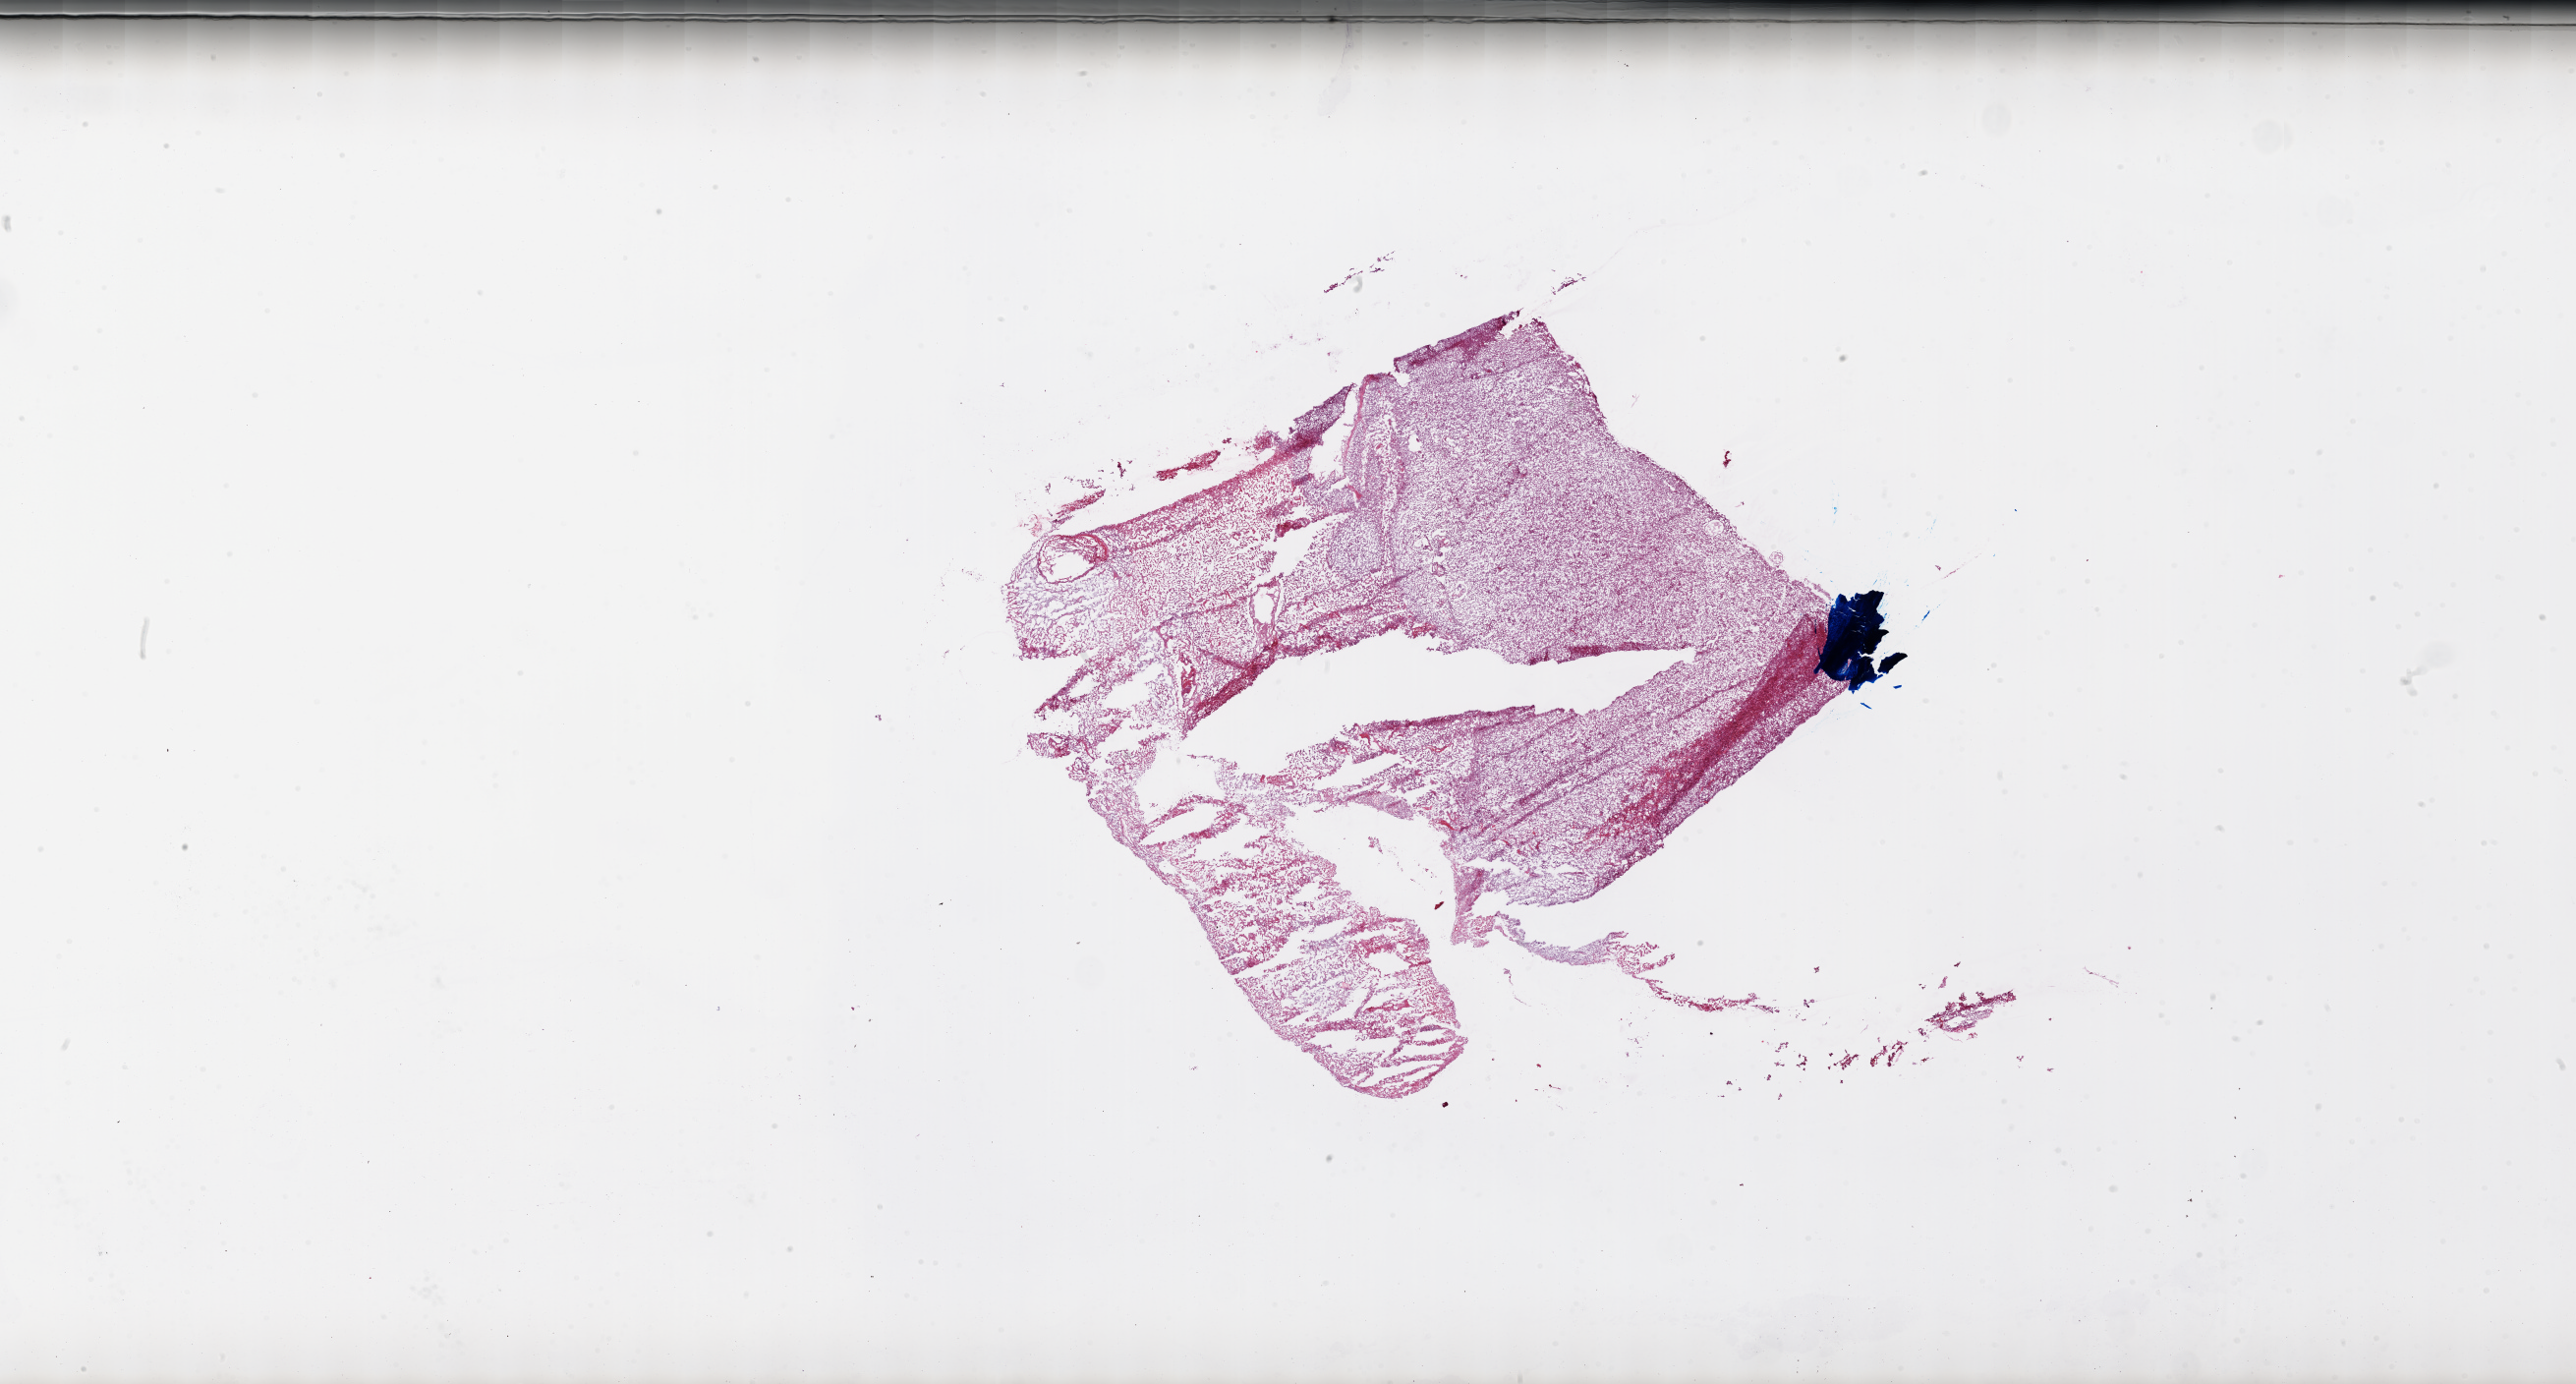
H&E whole-slide image — shown as a low-resolution overview of the whole scanned area (about 42.0 x 22.5 mm), frozen section from the top of the tissue portion, primary tumour sample from the brain. Patient: female, age at initial diagnosis 50 years. Pathologist review of this section (percent, as recorded): tumour cells 70%, tumour nuclei 100%, normal cells 0%, stromal cells 0%, necrosis 30%. Inflammatory infiltration, as recorded: lymphocyte infiltration 0%.
Diagnosis: Glioblastoma.